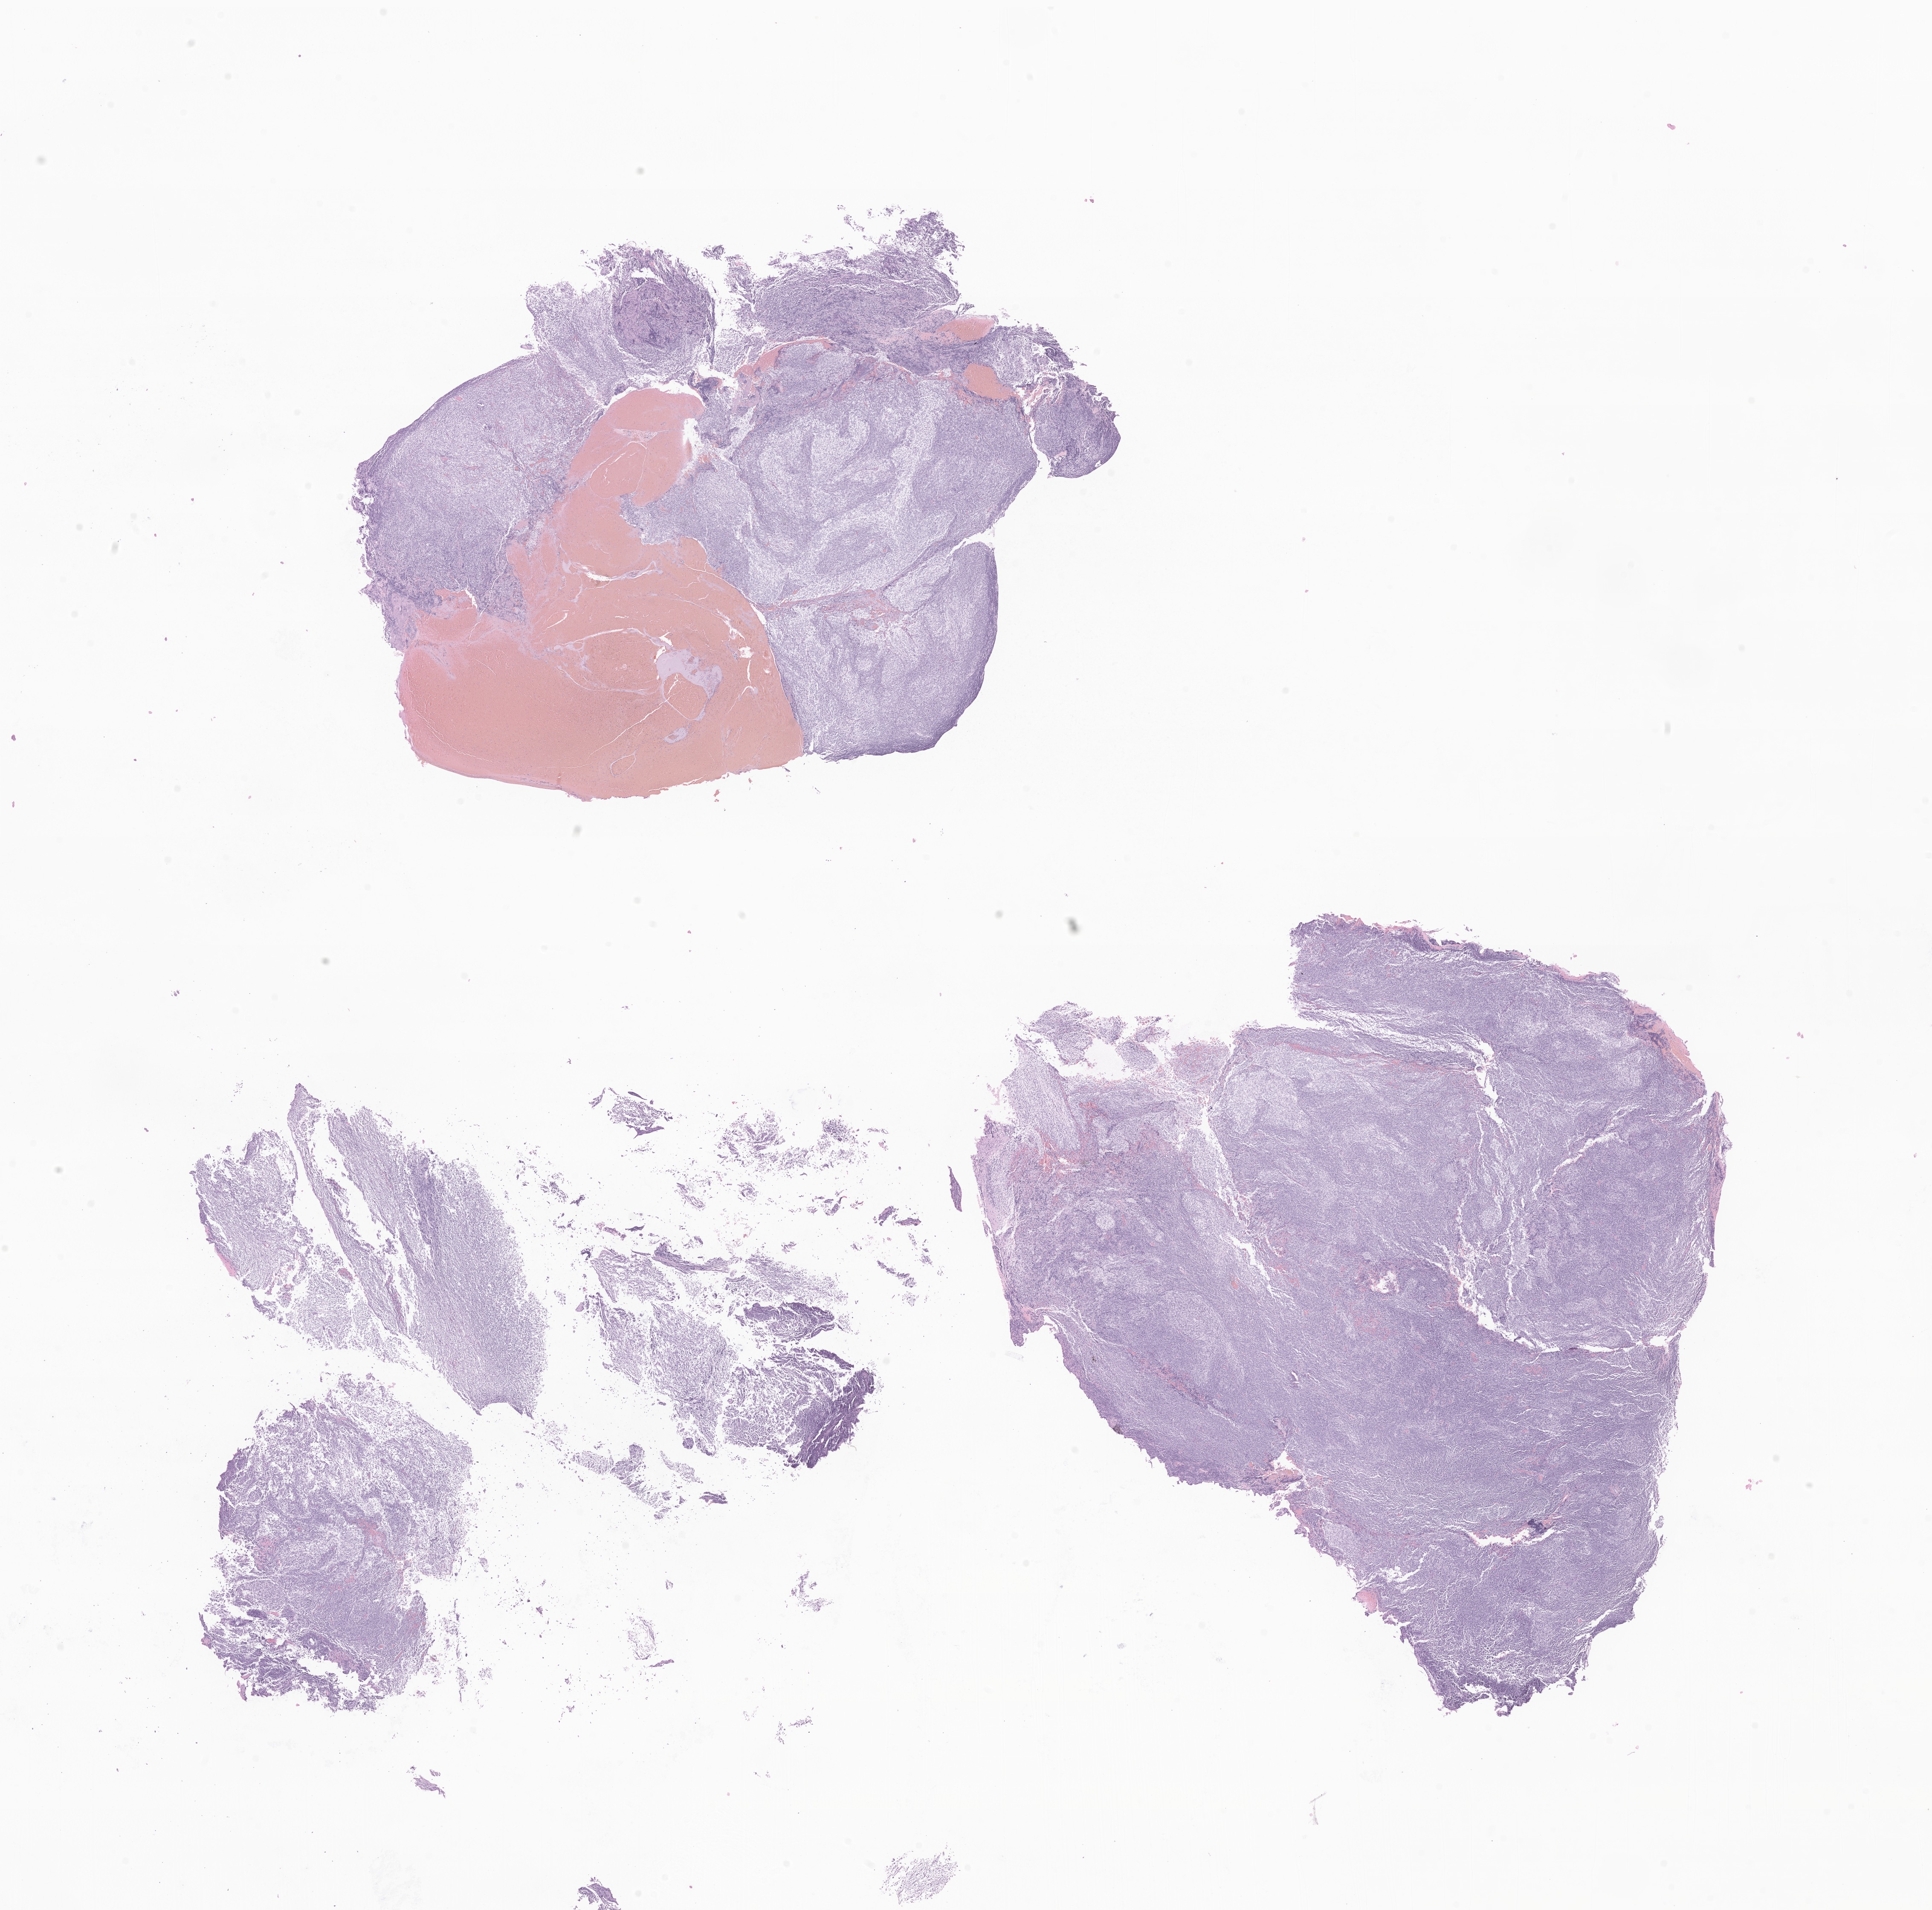
Digitized haematoxylin and eosin-stained section of tumor tissue from the brain — shown as a low-resolution overview of the whole scanned area (about 19.1 x 18.9 mm), formalin-fixed paraffin-embedded section. Patient male; age 329 days.
Recorded diagnosis: Desmoplastic nodular medulloblastoma.